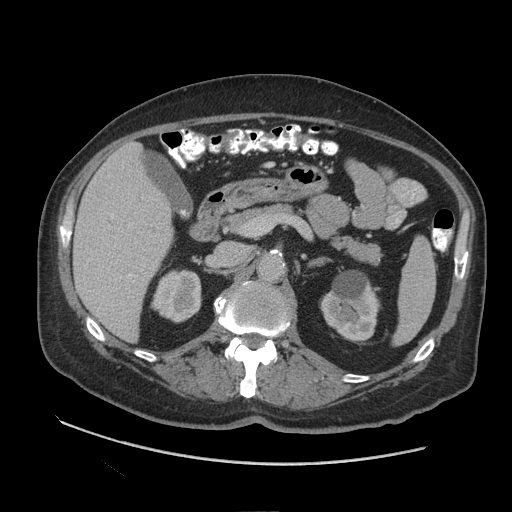
Contrast-enhanced abdominal CT (liver protocol), one axial slice. Reconstruction kernel STANDARD. 140 kVp. Soft-tissue window (W 400 / L 40 HU). 2.5 mm slice thickness. 512 × 512 image matrix, field of view 420 × 420 mm. From the clinical record (not read from this slice): diagnosis: hepatocellular carcinoma (patient treated with transarterial chemoembolisation; whether this scan precedes or follows treatment is not stated here); TNM stage (as recorded): Stage-I; Child-Pugh class: A; tumour nodularity: uninodular.
Annotated regions visible in this slice (semi-automatic segmentation, software-assisted and operator-edited):
- liver parenchyma outside the tumour (the mass and vessels are separate outlines, so this box may not span the whole liver): bounding box <72,142,172,340> (left, top, right, bottom; pixels)
- liver vessels: <111,214,136,278>